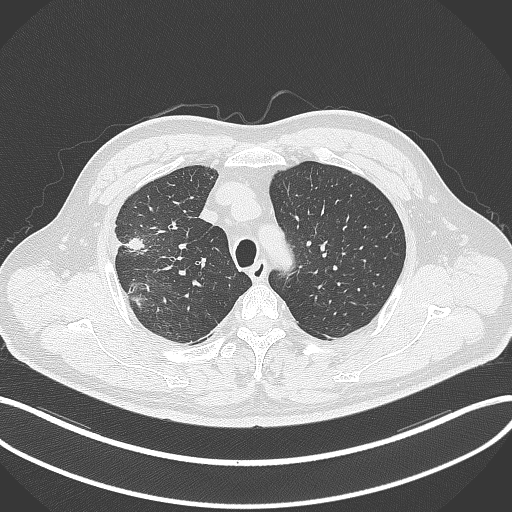
Chest CT, one axial slice. Slice 270 of 348 in the series (ordered by position). 120 kVp. Lung window (W 1500 / L -600 HU). 512 × 512 image matrix, field of view 400 × 400 mm. Patient: male, 55 years. Case-level facts recorded for this patient, not image findings: clinical TNM (as recorded): T3 N2 M1.
Annotated regions visible in this slice (rectangle marked by the reading radiologist):
- lung tumour (recorded histology: adenocarcinoma): box from (x=122, y=235) to (x=147, y=253) px